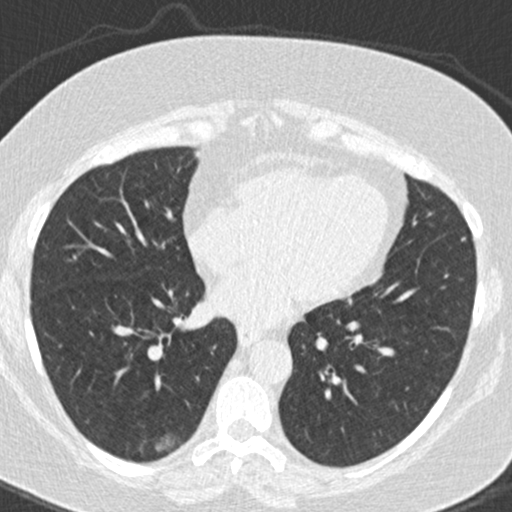
Low-dose screening chest CT, one axial slice; position 70 of 177 along the scan axis; lung window (W 1500 / L -600 HU); 512 × 512 image matrix, field of view 300 × 300 mm.
Structures marked on this image (outlined manually by an expert reader):
- lesion 1 (tumor, lower lobe of right lung): bounding box [x1, y1, x2, y2] px = [155, 433, 176, 453]